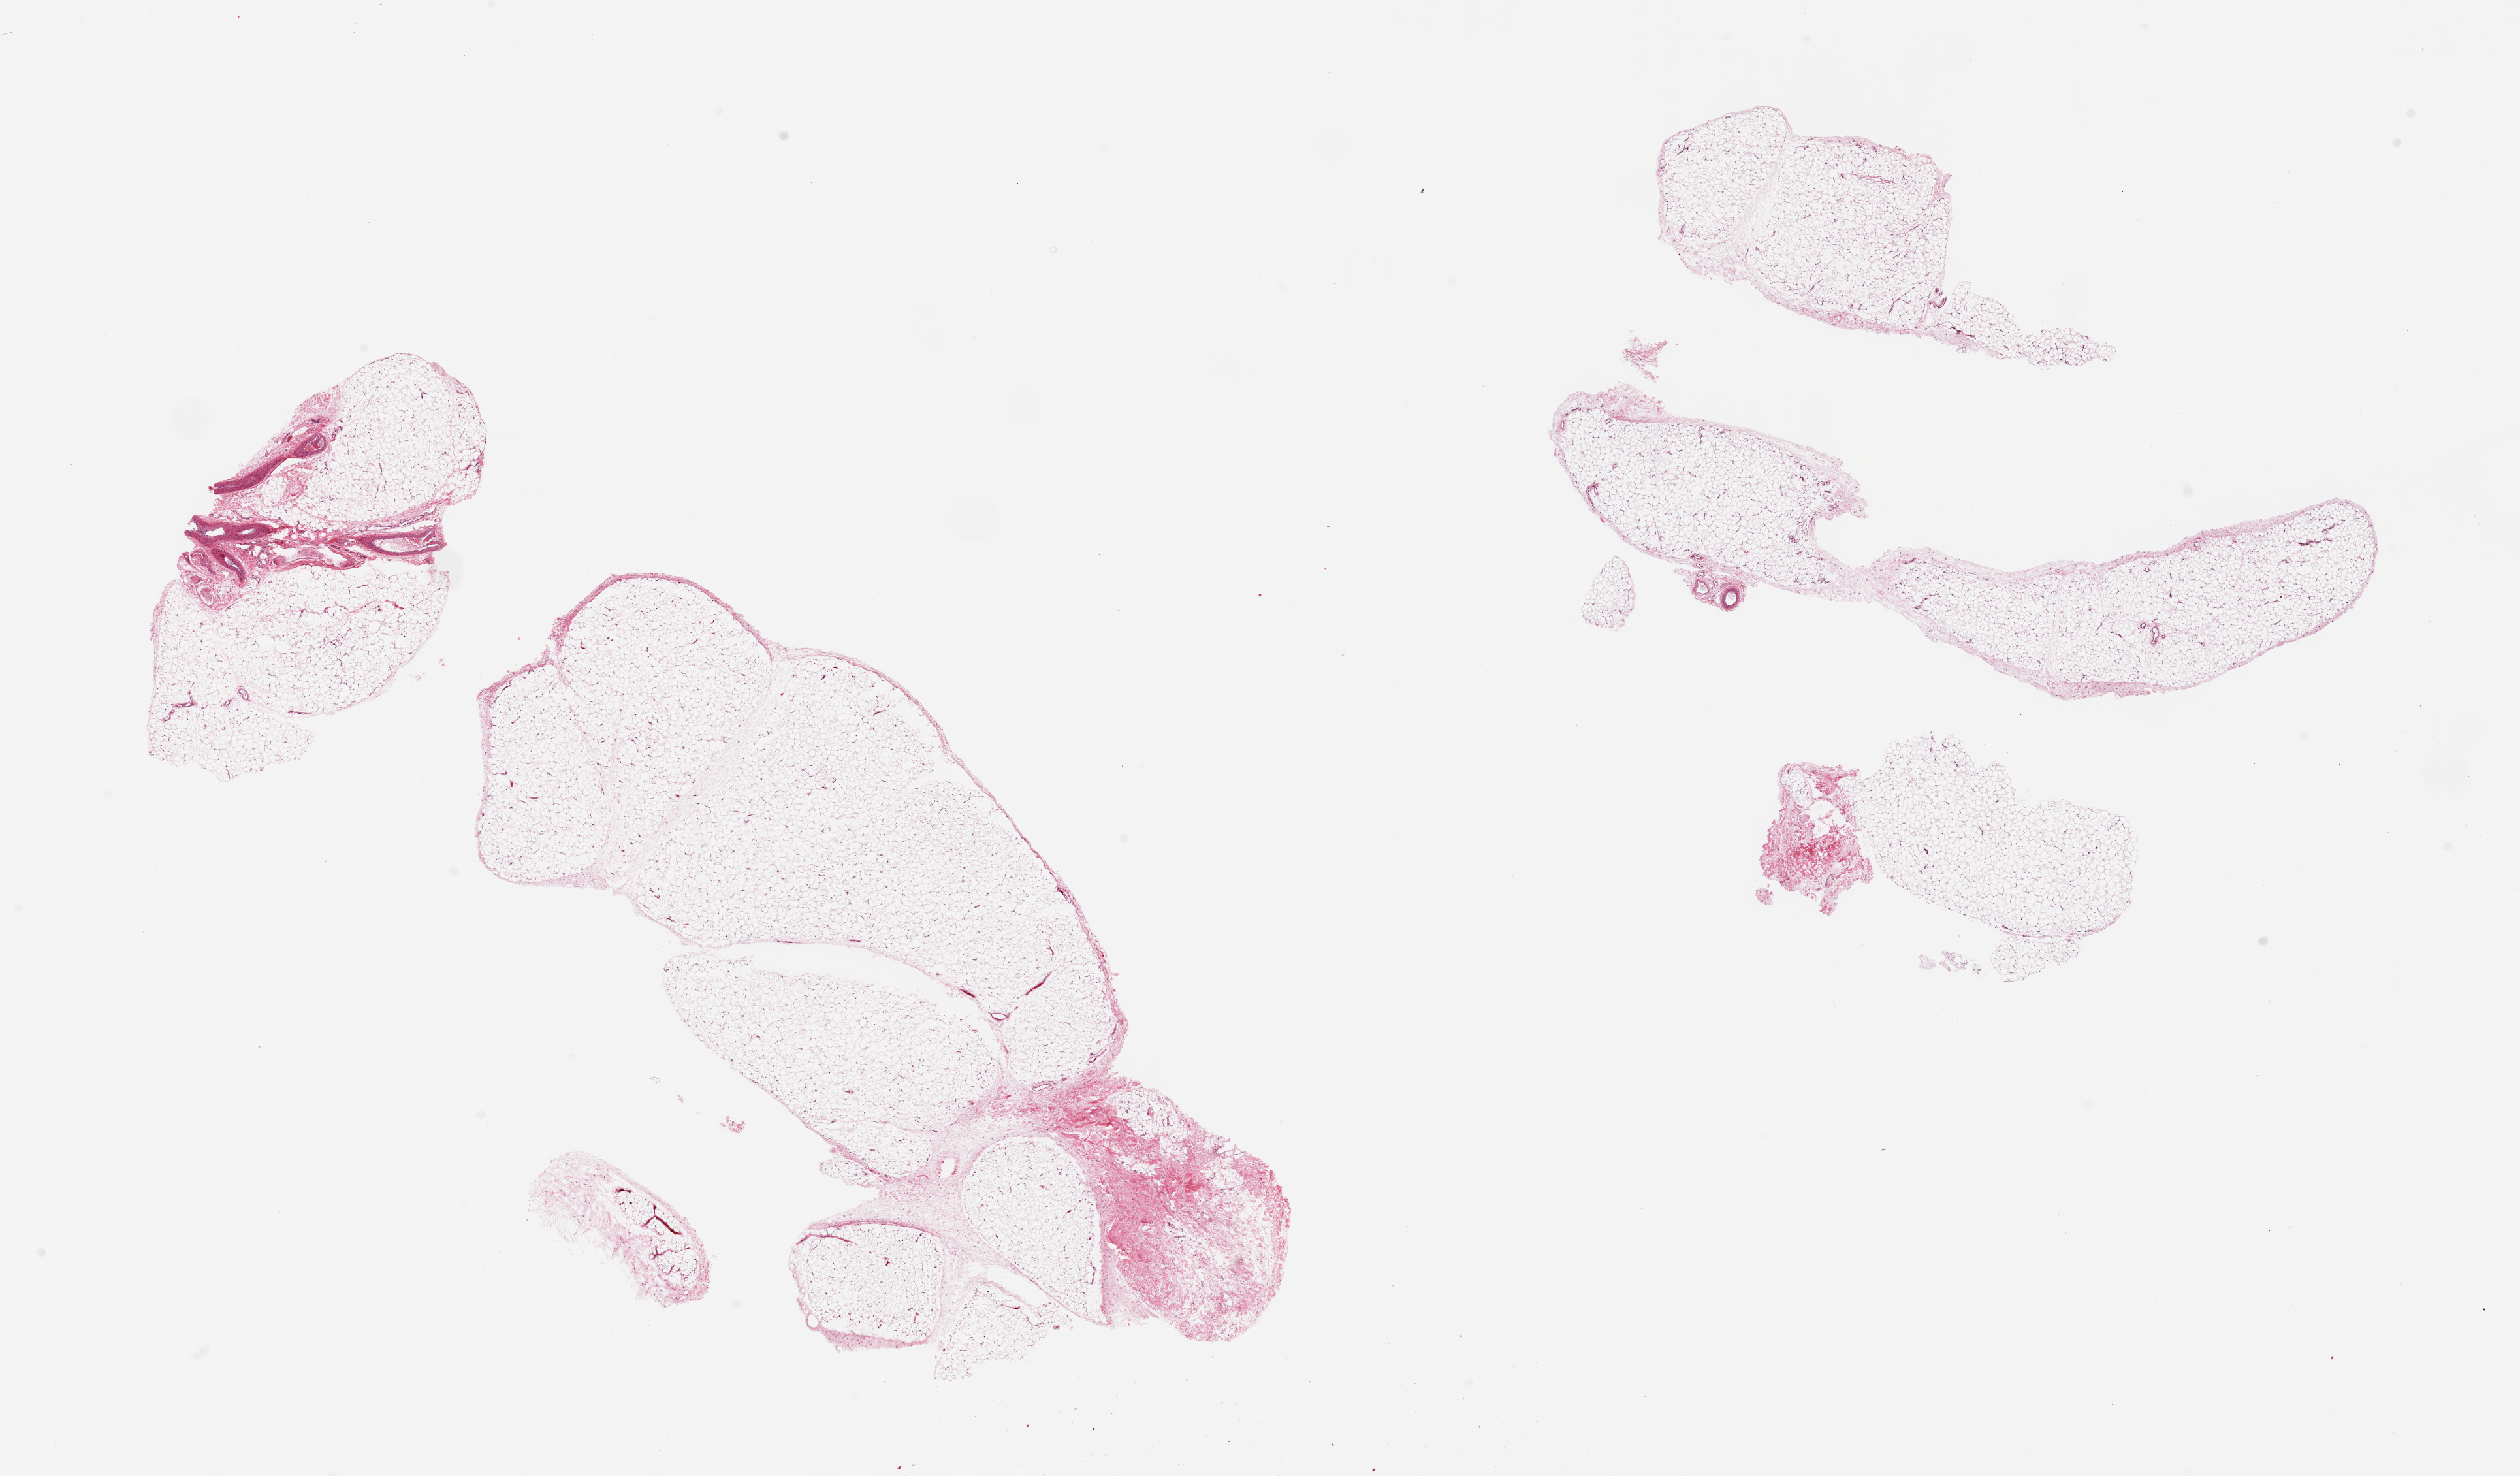
Whole-slide image, hematoxylin and eosin (H&E) stain — a low-resolution overview of the entire scanned area, about 30.5 x 17.9 mm. PAXgene-fixed paraffin-embedded (PFPE) section. Sampled site (target tissue): adipose tissue. Tissue donor sample.
Pathologist's review note for this sample: 2 pieces ~10-15% fascial/fibrous tissue.